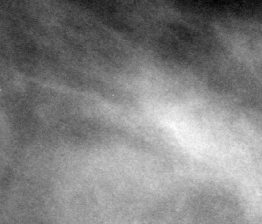
Crop from a digitized film mammogram around one marked abnormality; left breast; CC view; BI-RADS breast density category 3 (scale 1–4).
Marked abnormality: mass, shape round, margins circumscribed; BI-RADS assessment category 3; pathology (as recorded): benign.